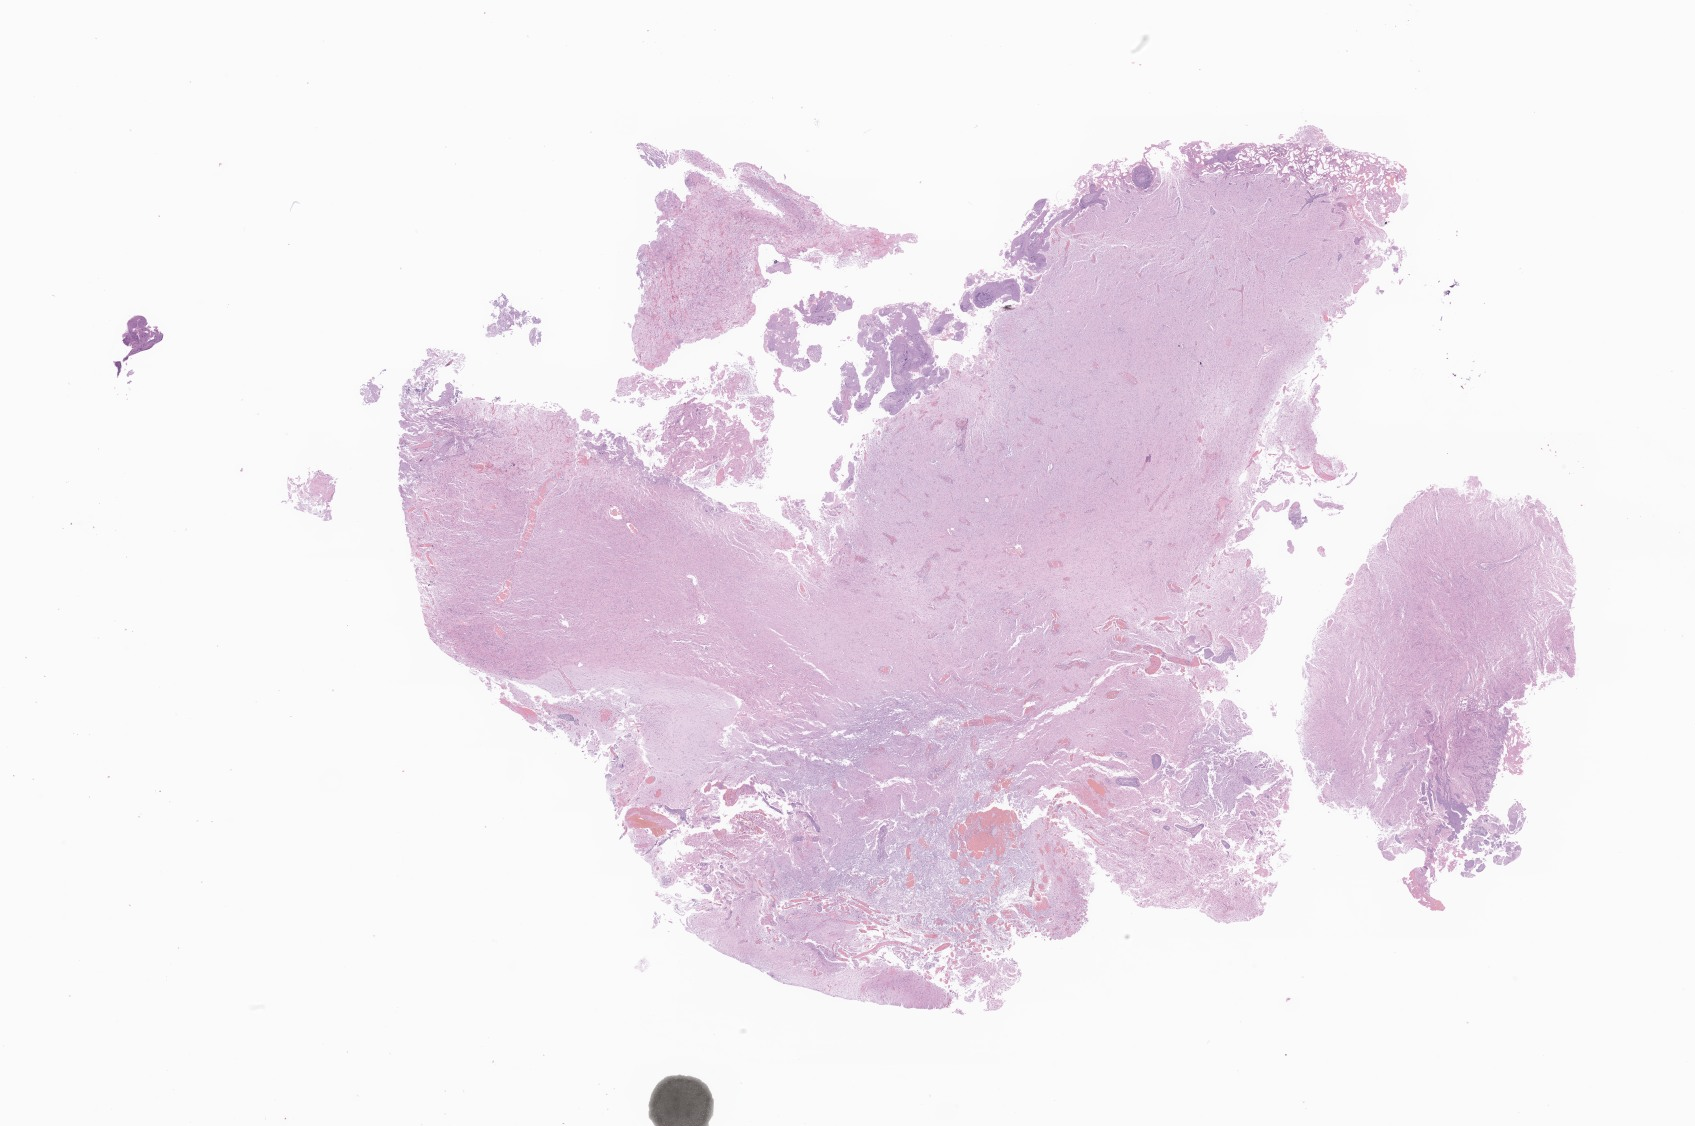
Whole-slide image, H&E stain of tumor tissue from the brain — a low-resolution overview of the entire scanned area, about 28.6 x 19.0 mm. FFPE section. Patient: male, age 98 months.
Diagnosis: Pilocytic astrocytoma.